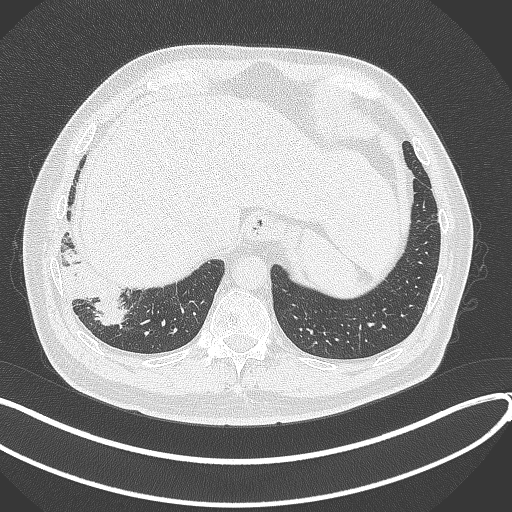
Chest CT, one axial slice. Slice 58 of 360 in the series (ordered by position). Lung window (W 1500 / L -600 HU). 1 mm slice thickness. 512 × 512 image matrix, field of view 400 × 400 mm. Patient: male, 59 years.
Outlined on this slice (rectangle marked by the reading radiologist):
- lung tumour (recorded histology: adenocarcinoma): box from (x=63, y=254) to (x=128, y=330) px